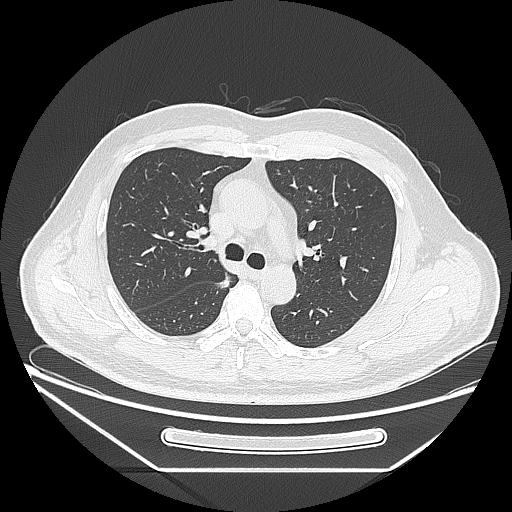
Chest CT, one axial slice; slice 167 of 271 in the series (ordered by position); reconstruction kernel LUNG; 120 kVp; lung window (W 1500 / L -600 HU); 1.25 mm slice thickness; 512 × 512 image matrix, field of view 414 × 414 mm. Male patient, age 49 years. From the clinical record (not read from this slice): clinical TNM (as recorded): T1b N0 M0; histopathological grade: G2.
Structures marked on this image (bounding box drawn by a radiologist):
- lung tumour (recorded histology: adenocarcinoma): box from (x=211, y=268) to (x=233, y=292) px